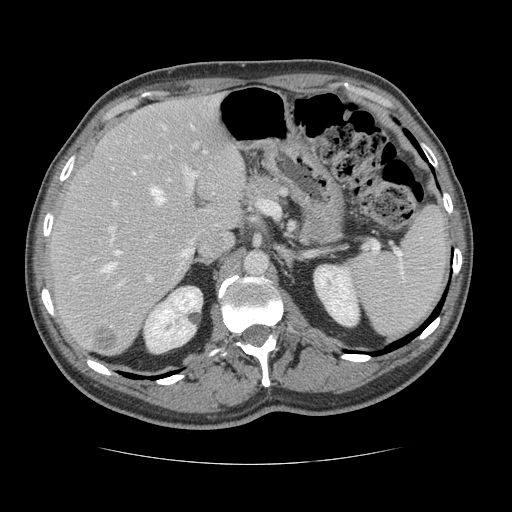
Contrast-enhanced abdominal CT, one axial slice; slice 84 of 134 in the series (ordered by position); reconstruction kernel STANDARD; intravenous contrast given; soft-tissue window (W 400 / L 40 HU); 512 × 512 image matrix. Male patient, age 68 years. From the clinical record (not read from this slice): diagnosis: colorectal cancer liver metastases, imaged before liver resection; multiple liver metastases: yes; largest metastasis: 2.2 cm; disease in both lobes: no.
Structures marked on this image (manually delineated by an expert):
- hepatic veins: bounding box (x1, y1, x2, y2) in pixels: (102, 125, 214, 273)
- liver: (51, 95, 247, 355)
- planned liver remnant (the part of the liver to remain after resection): (51, 95, 247, 337)
- portal vein (with intrahepatic branches): (109, 124, 199, 281)
- liver metastasis: (95, 328, 118, 352)